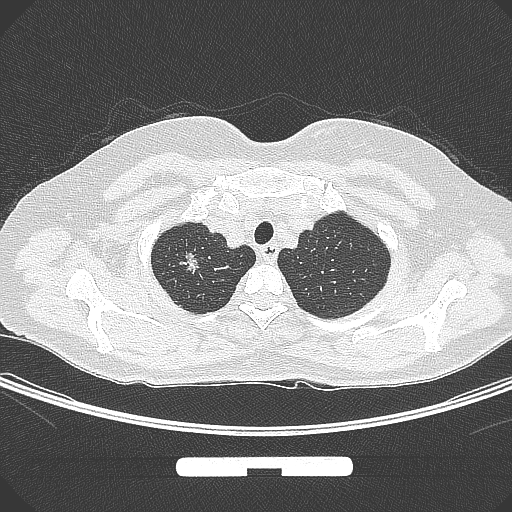
Chest CT, one axial slice; slice 259 of 295 in the series (ordered by position); lung window (W 1500 / L -600 HU); 512 × 512 image matrix, field of view 369 × 369 mm. Patient: female, 58 years. From the clinical record (not read from this slice): clinical TNM (as recorded): T1b N0 M0.
Annotated regions visible in this slice (bounding box drawn by a radiologist):
- lung tumour (recorded histology: adenocarcinoma): bounding box (x1, y1, x2, y2) in pixels: (176, 245, 203, 283)